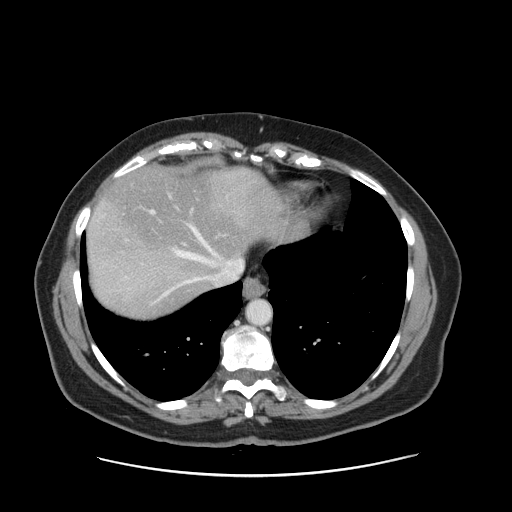
Contrast-enhanced abdominal CT, one axial slice. Slice 132 of 161 in the series (ordered by position). 120 kVp. Intravenous contrast given. Soft-tissue window (W 400 / L 40 HU). 512 × 512 image matrix, field of view 398 × 398 mm. Female patient, age 62 years. From the clinical record (not read from this slice): diagnosis: colorectal cancer liver metastases, imaged before liver resection; multiple liver metastases: no; largest metastasis: 2.5 cm; disease in both lobes: no.
Structures marked on this image (outlined manually by an expert reader):
- hepatic veins: bounding box (x1, y1, x2, y2) in pixels: (124, 190, 243, 295)
- liver: (87, 166, 287, 318)
- planned liver remnant (the part of the liver to remain after resection): (95, 167, 286, 278)
- portal vein (with intrahepatic branches): (151, 192, 183, 244)